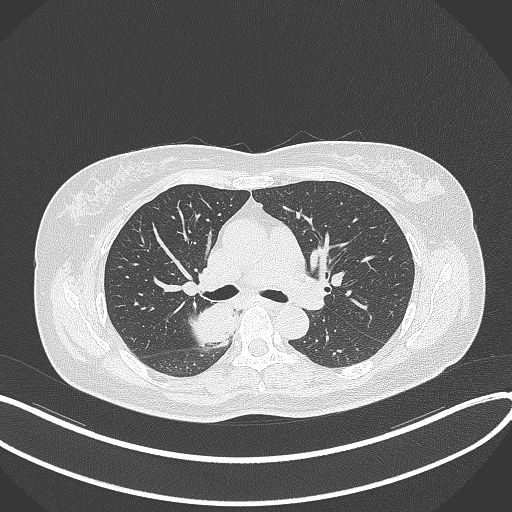
Chest CT, one axial slice. Slice 227 of 331 in the series (ordered by position). Lung window (W 1500 / L -600 HU). 1 mm slice thickness. 512 × 512 image matrix, field of view 400 × 400 mm. Female patient, age 54 years. From the clinical record (not read from this slice): clinical TNM (as recorded): T4 N0 M0.
Structures marked on this image (bounding box drawn by a radiologist):
- lung tumour (recorded histology: adenocarcinoma): bounding box [x1, y1, x2, y2] px = [190, 298, 238, 349]